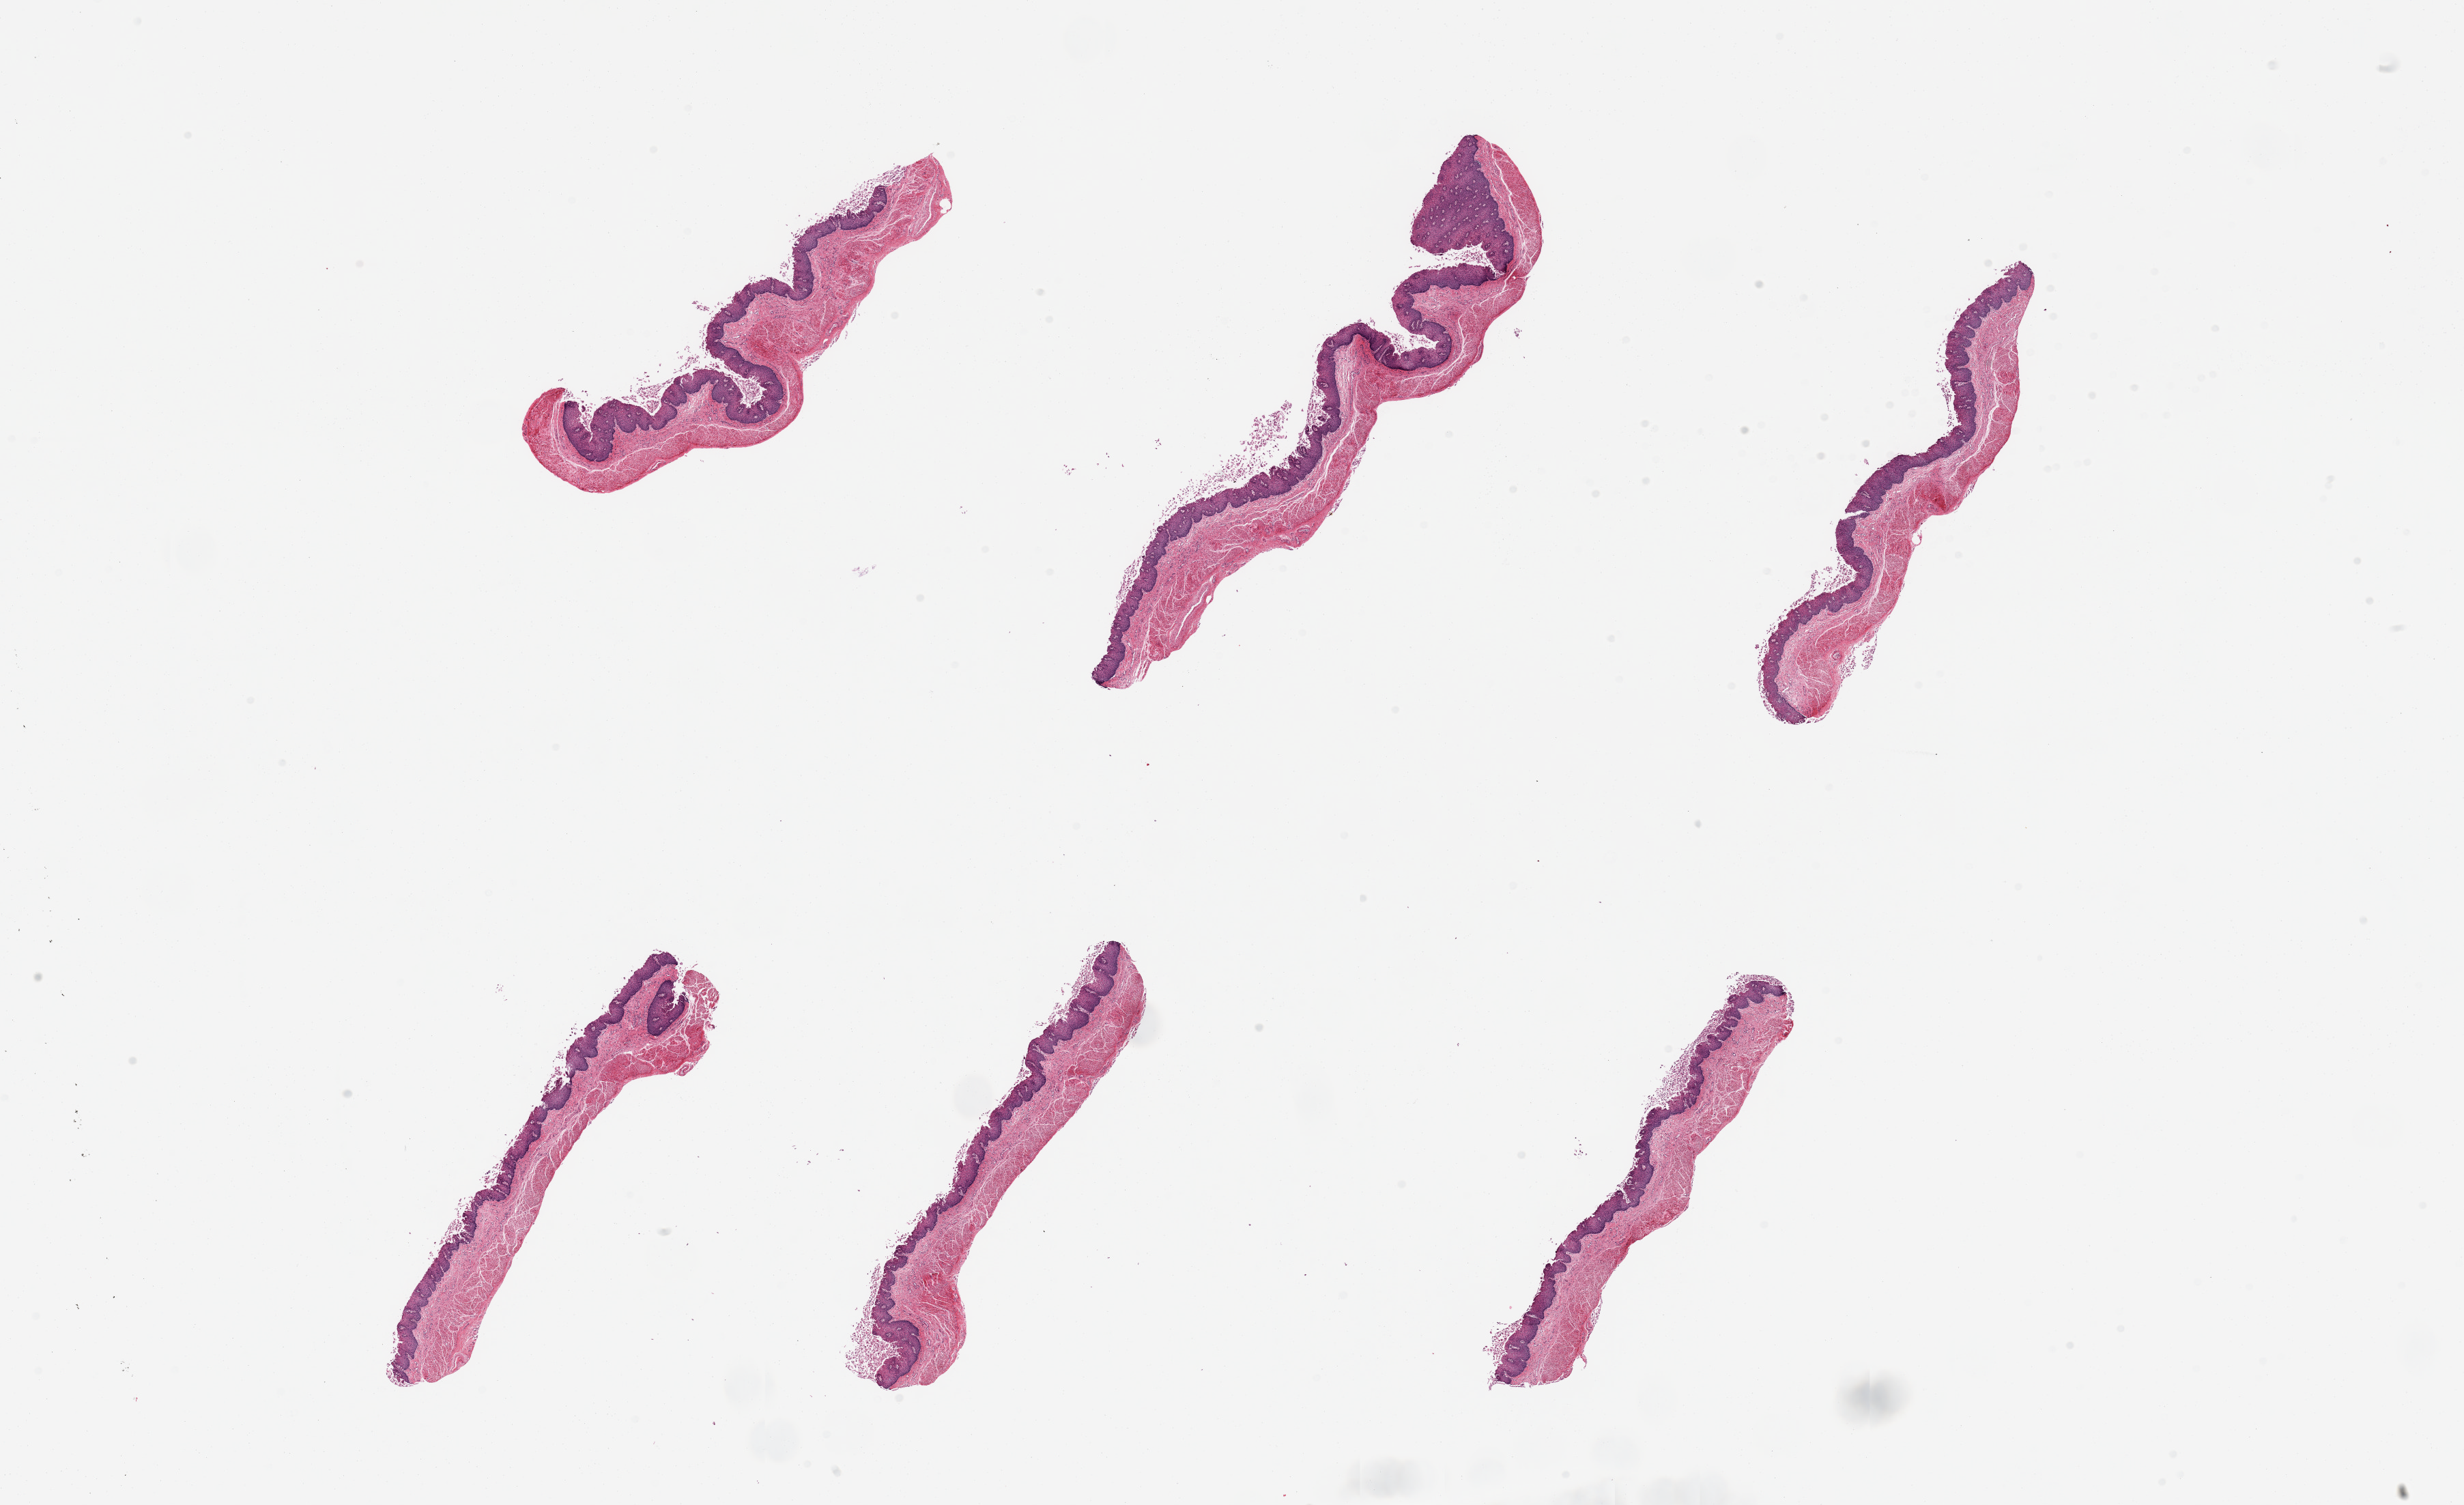
Digitized haematoxylin and eosin-stained section, shown as a low-resolution overview of the whole scanned area (about 28.5 x 17.4 mm). PAXgene-fixed, paraffin-embedded tissue. Section of esophageal mucous membrane (target tissue). Donor tissue sample. Donor sex: female.
Pathologist's review note for this sample: 6 pieces; focal surface desquamation.